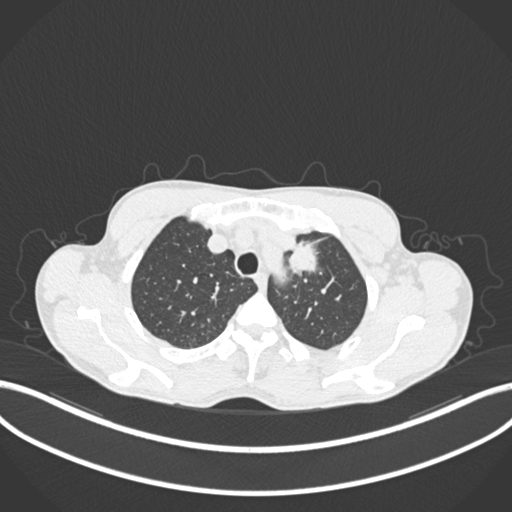
Chest CT, one axial slice; slice 169 of 211 in the series (ordered by position); 120 kVp; lung window (W 1500 / L -600 HU); 1 mm slice thickness; 512 × 512 image matrix, field of view 400 × 400 mm. Patient: male, 58 years. From the clinical record (not read from this slice): clinical TNM (as recorded): T1c N1 M0.
Annotated regions visible in this slice (bounding box drawn by a radiologist):
- lung tumour (recorded histology: adenocarcinoma): bounding box (x1, y1, x2, y2) in pixels: (281, 231, 326, 277)